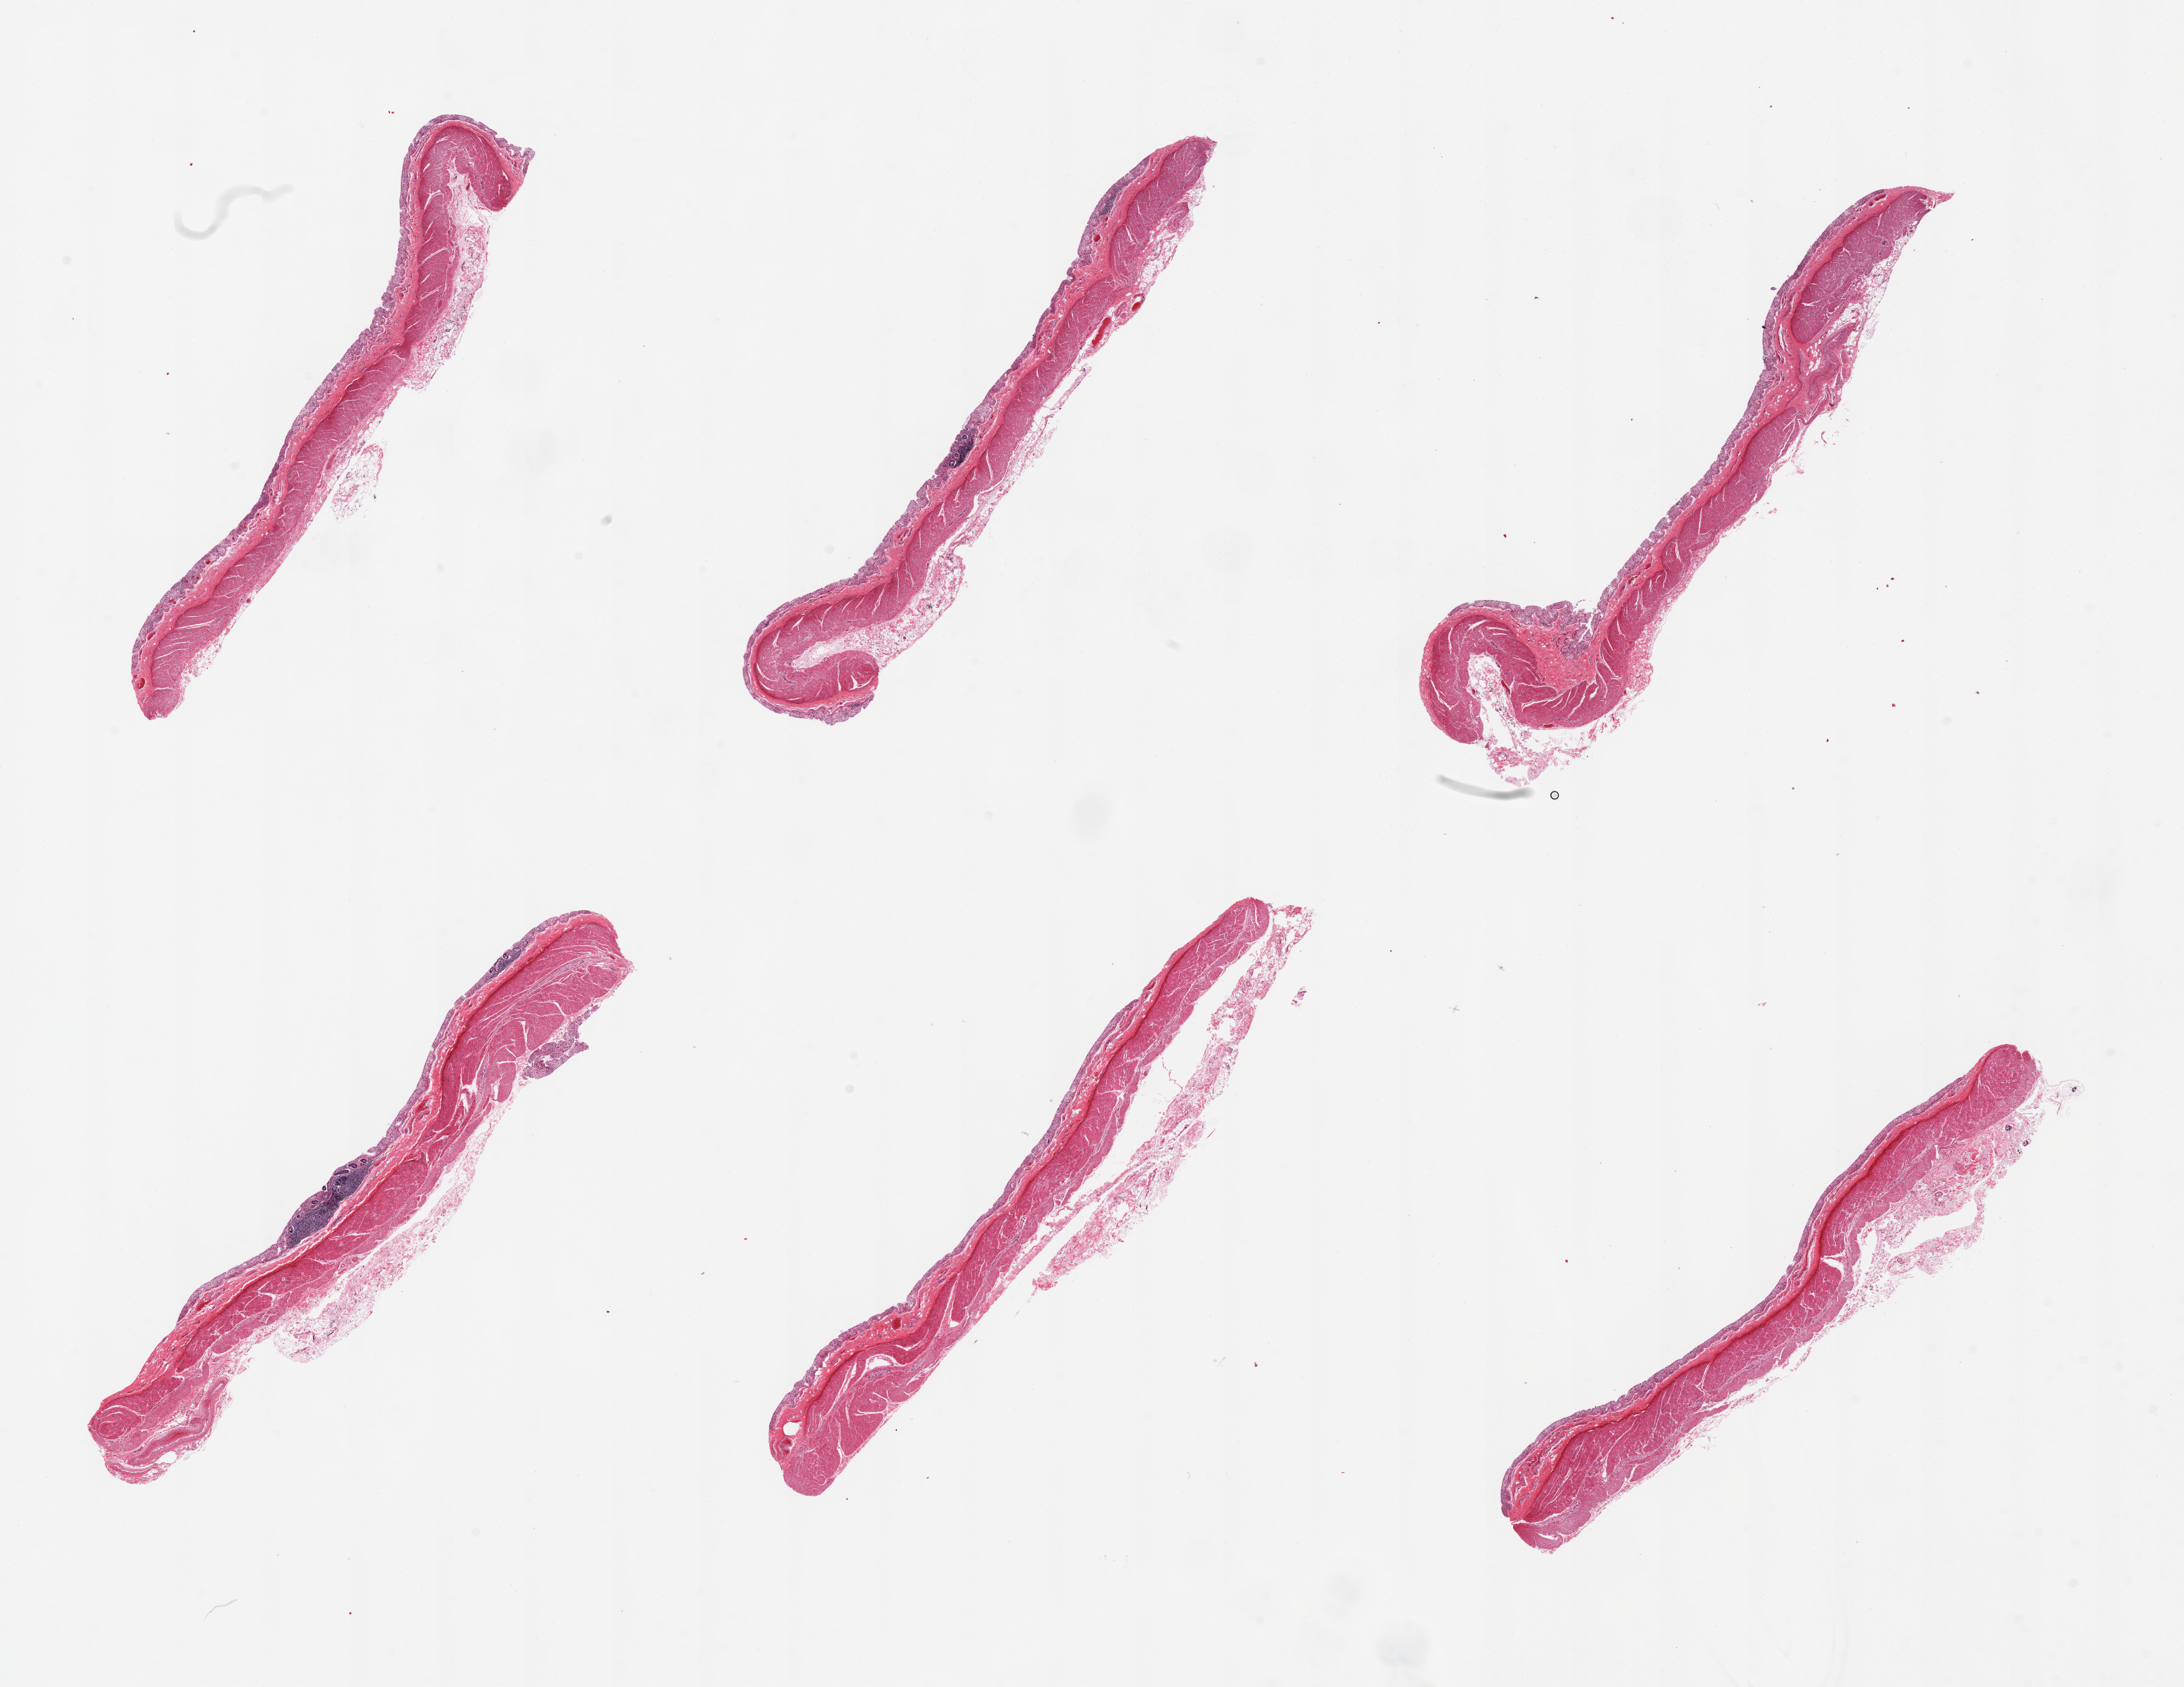
Whole-slide image, haematoxylin and eosin stain, brightfield, a low-resolution overview of the entire scanned area, about 24.6 x 19.0 mm. Donor sex: female.
* specimen: PAXgene-fixed, paraffin-embedded tissue; section of transverse colon (target tissue); tissue donor sample